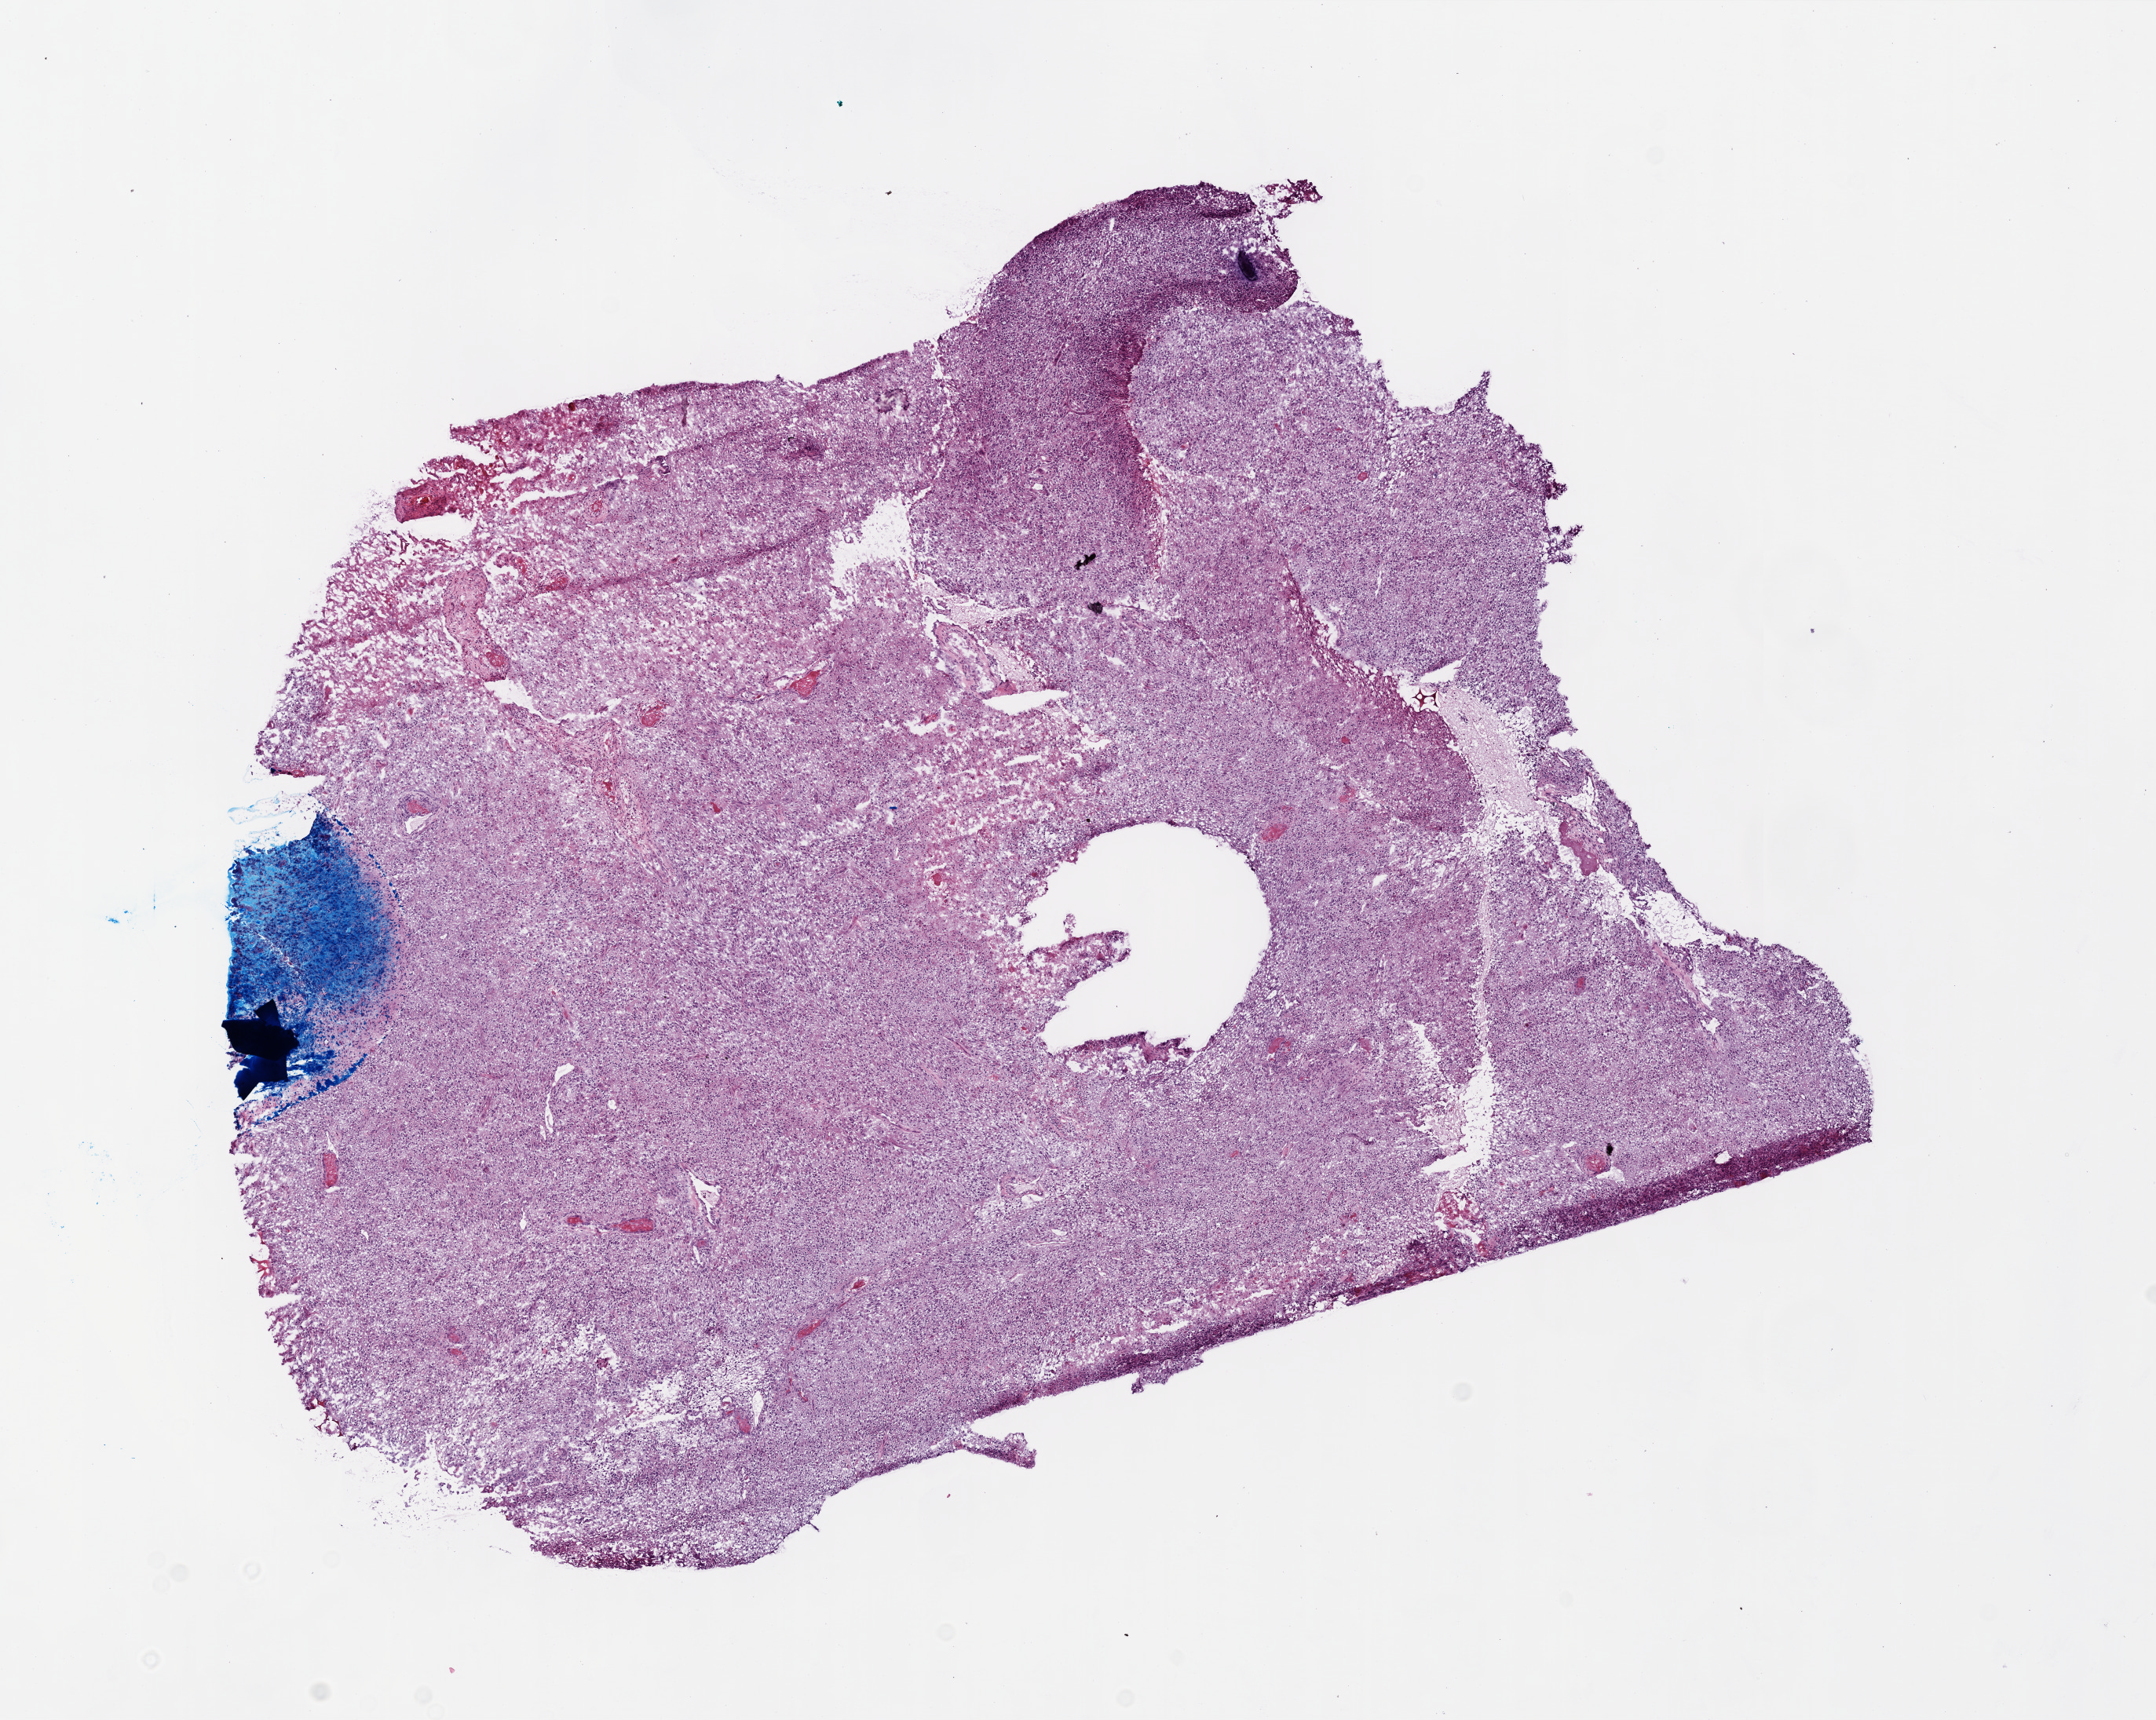
Digitized Hematoxylin and eosin (H&E) stained tissue section (whole slide), shown as a low-resolution overview of the whole scanned area (about 11.0 x 8.8 mm), frozen section from the top of the tissue portion, primary tumour sample from the brain. Patient: male, age at initial diagnosis 78 years. Slide review estimates, as recorded: tumour cells 95%, tumour nuclei 95%, normal cells 0%, stromal cells 0%, necrosis 5%.
Diagnosis: Glioblastoma.